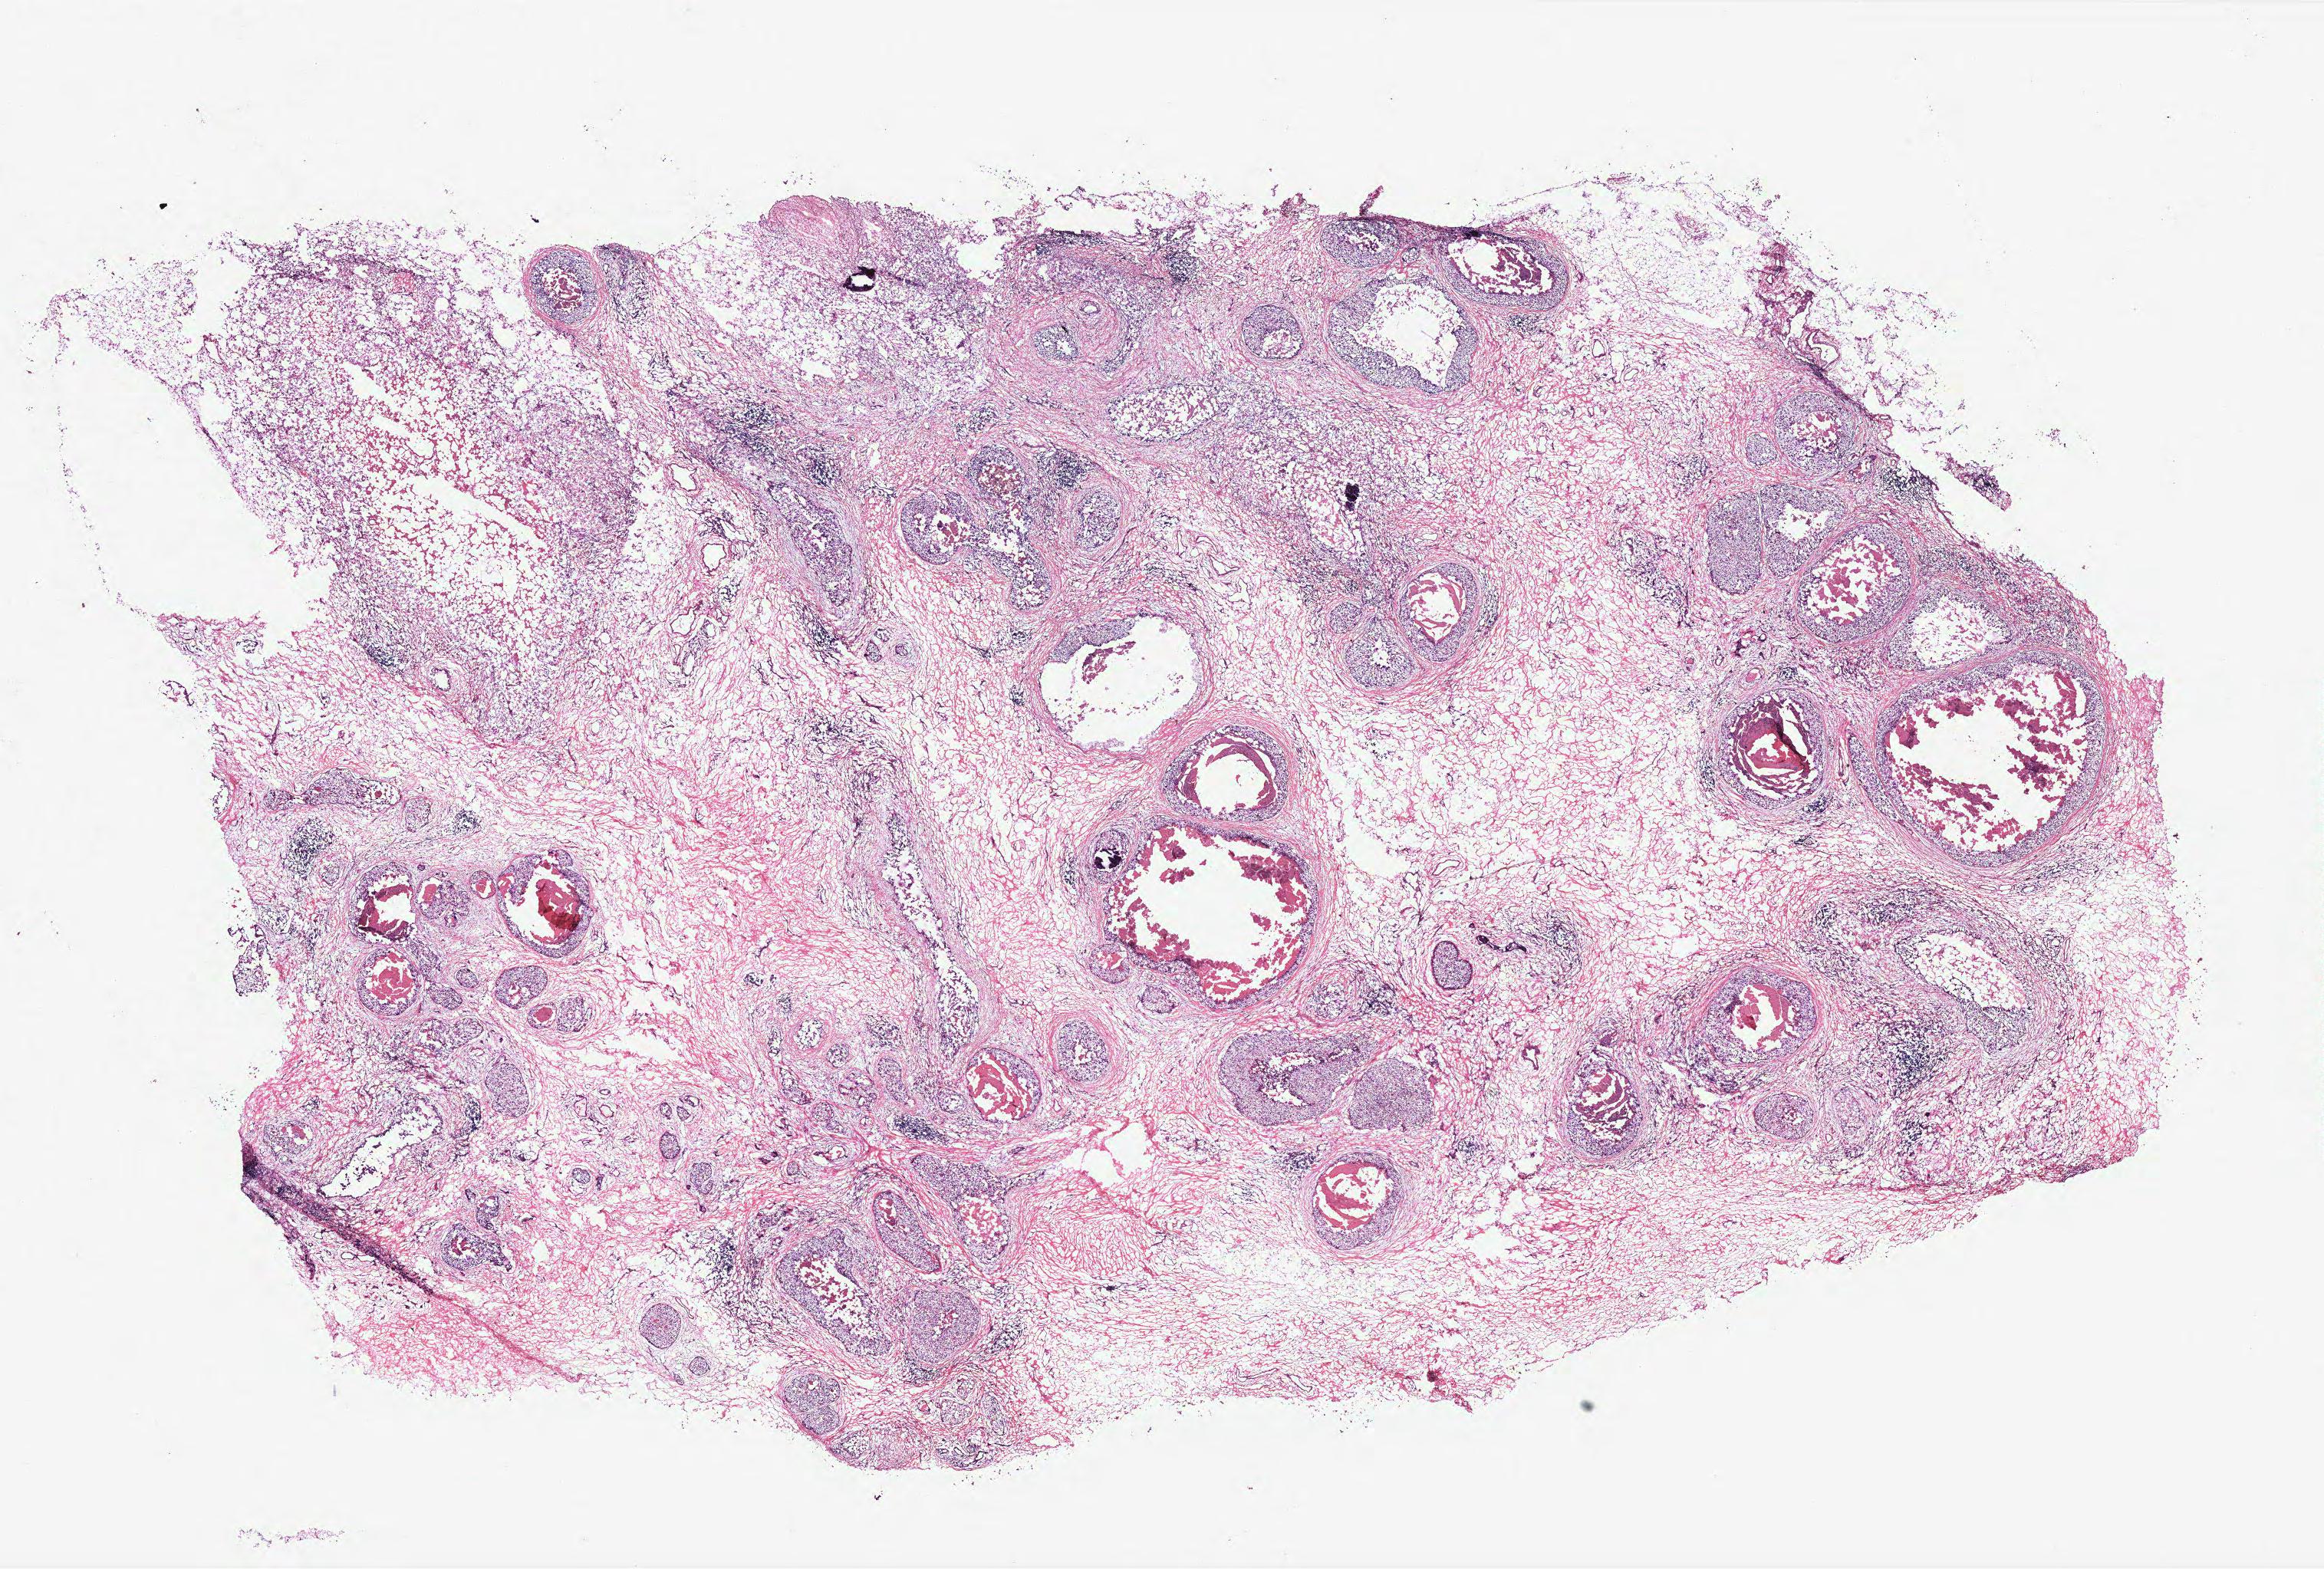
Digitized H&E tissue section (whole slide) — whole scanned area (about 24.2 x 16.4 mm) shown as a low-resolution overview, breast, tissue type not recorded. Female, 47 y/o.
Patient diagnosis: Infiltrating duct carcinoma, NOS.